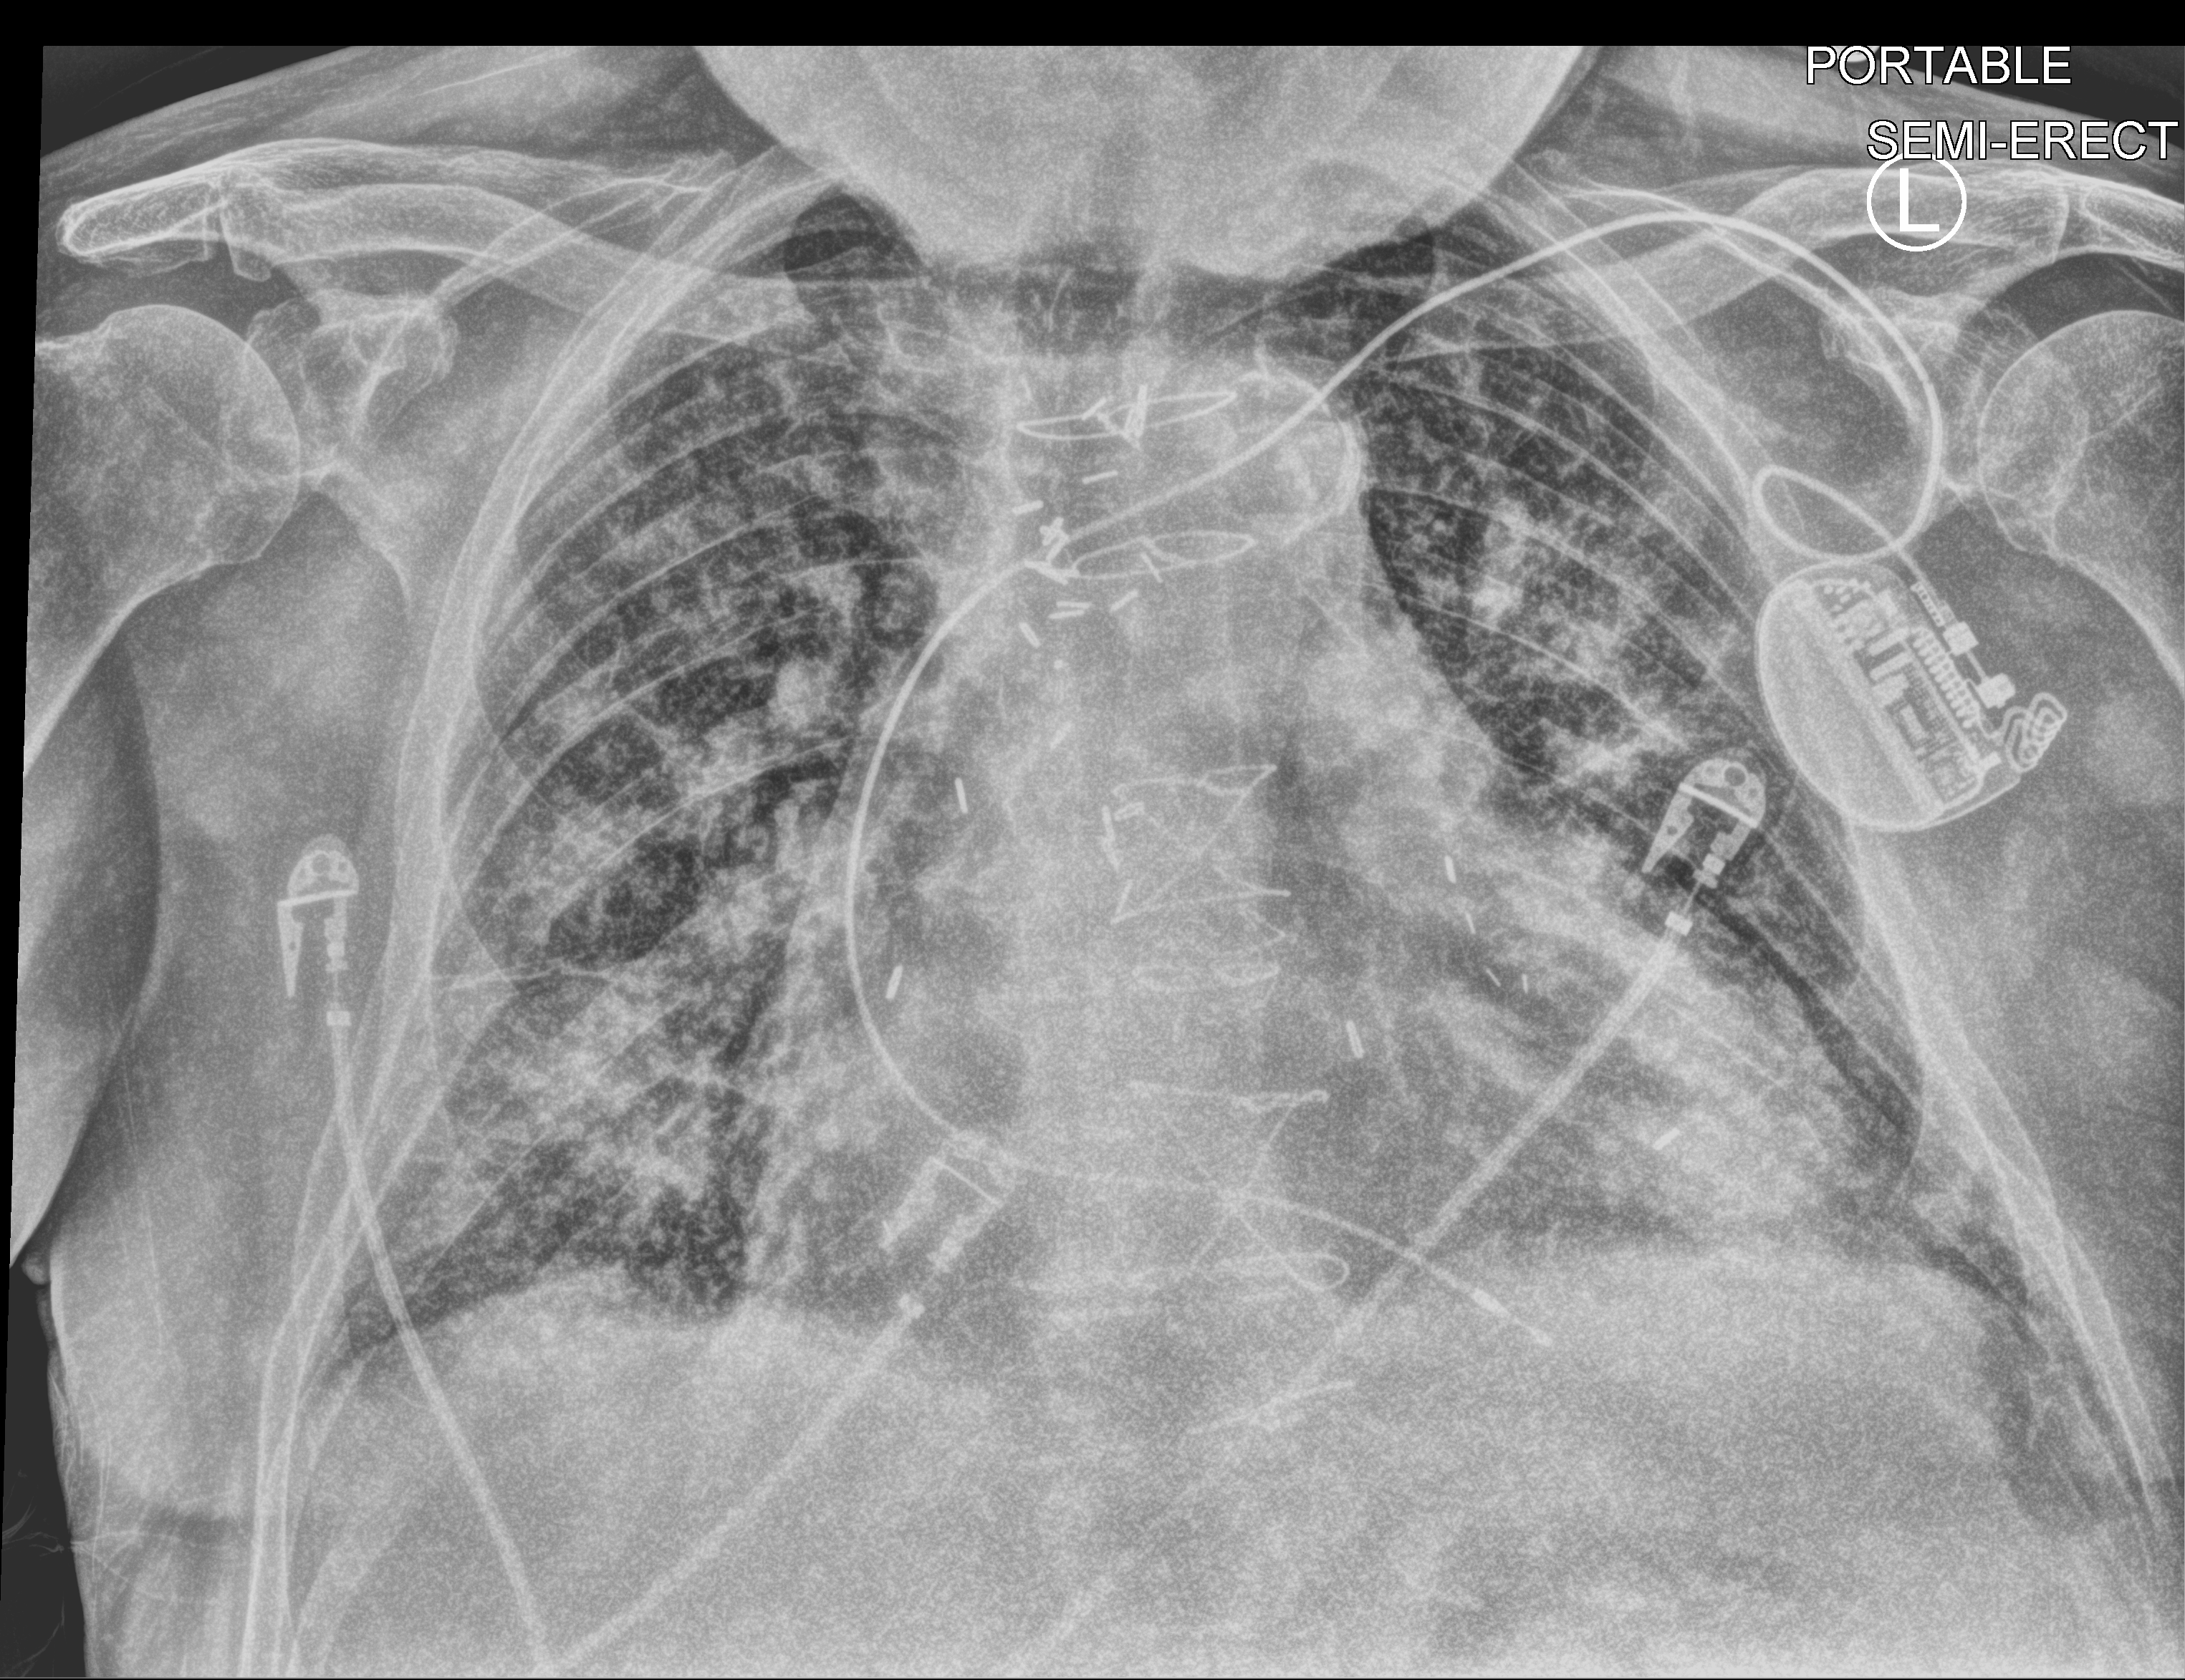
Bedside chest radiograph (computed radiography), anteroposterior (AP) projection. Male patient hospitalised with COVID-19, age 75–90 years.
Admission-level facts for this patient (not findings on this image; timing relative to this image not recorded):
- admitted to intensive care during this hospital stay: yes